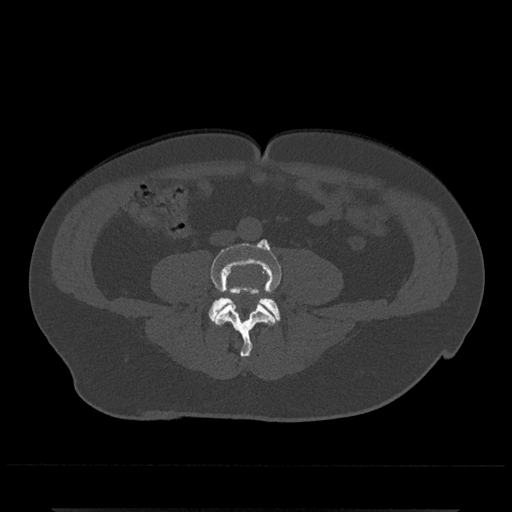
CT including the spine, one axial slice; 120 kVp; bone window (W 1800 / L 400 HU); 512 × 512 image matrix, field of view 393 × 393 mm. Male patient, age 67 years. From the clinical record (not read from this slice): primary cancer: prostate.
Annotated regions visible in this slice (semi-automatic segmentation, software-assisted and operator-edited):
- L4 vertebra: bounding box [x1, y1, x2, y2] px = [210, 239, 282, 358]
- L5 vertebra: [208, 297, 281, 321]